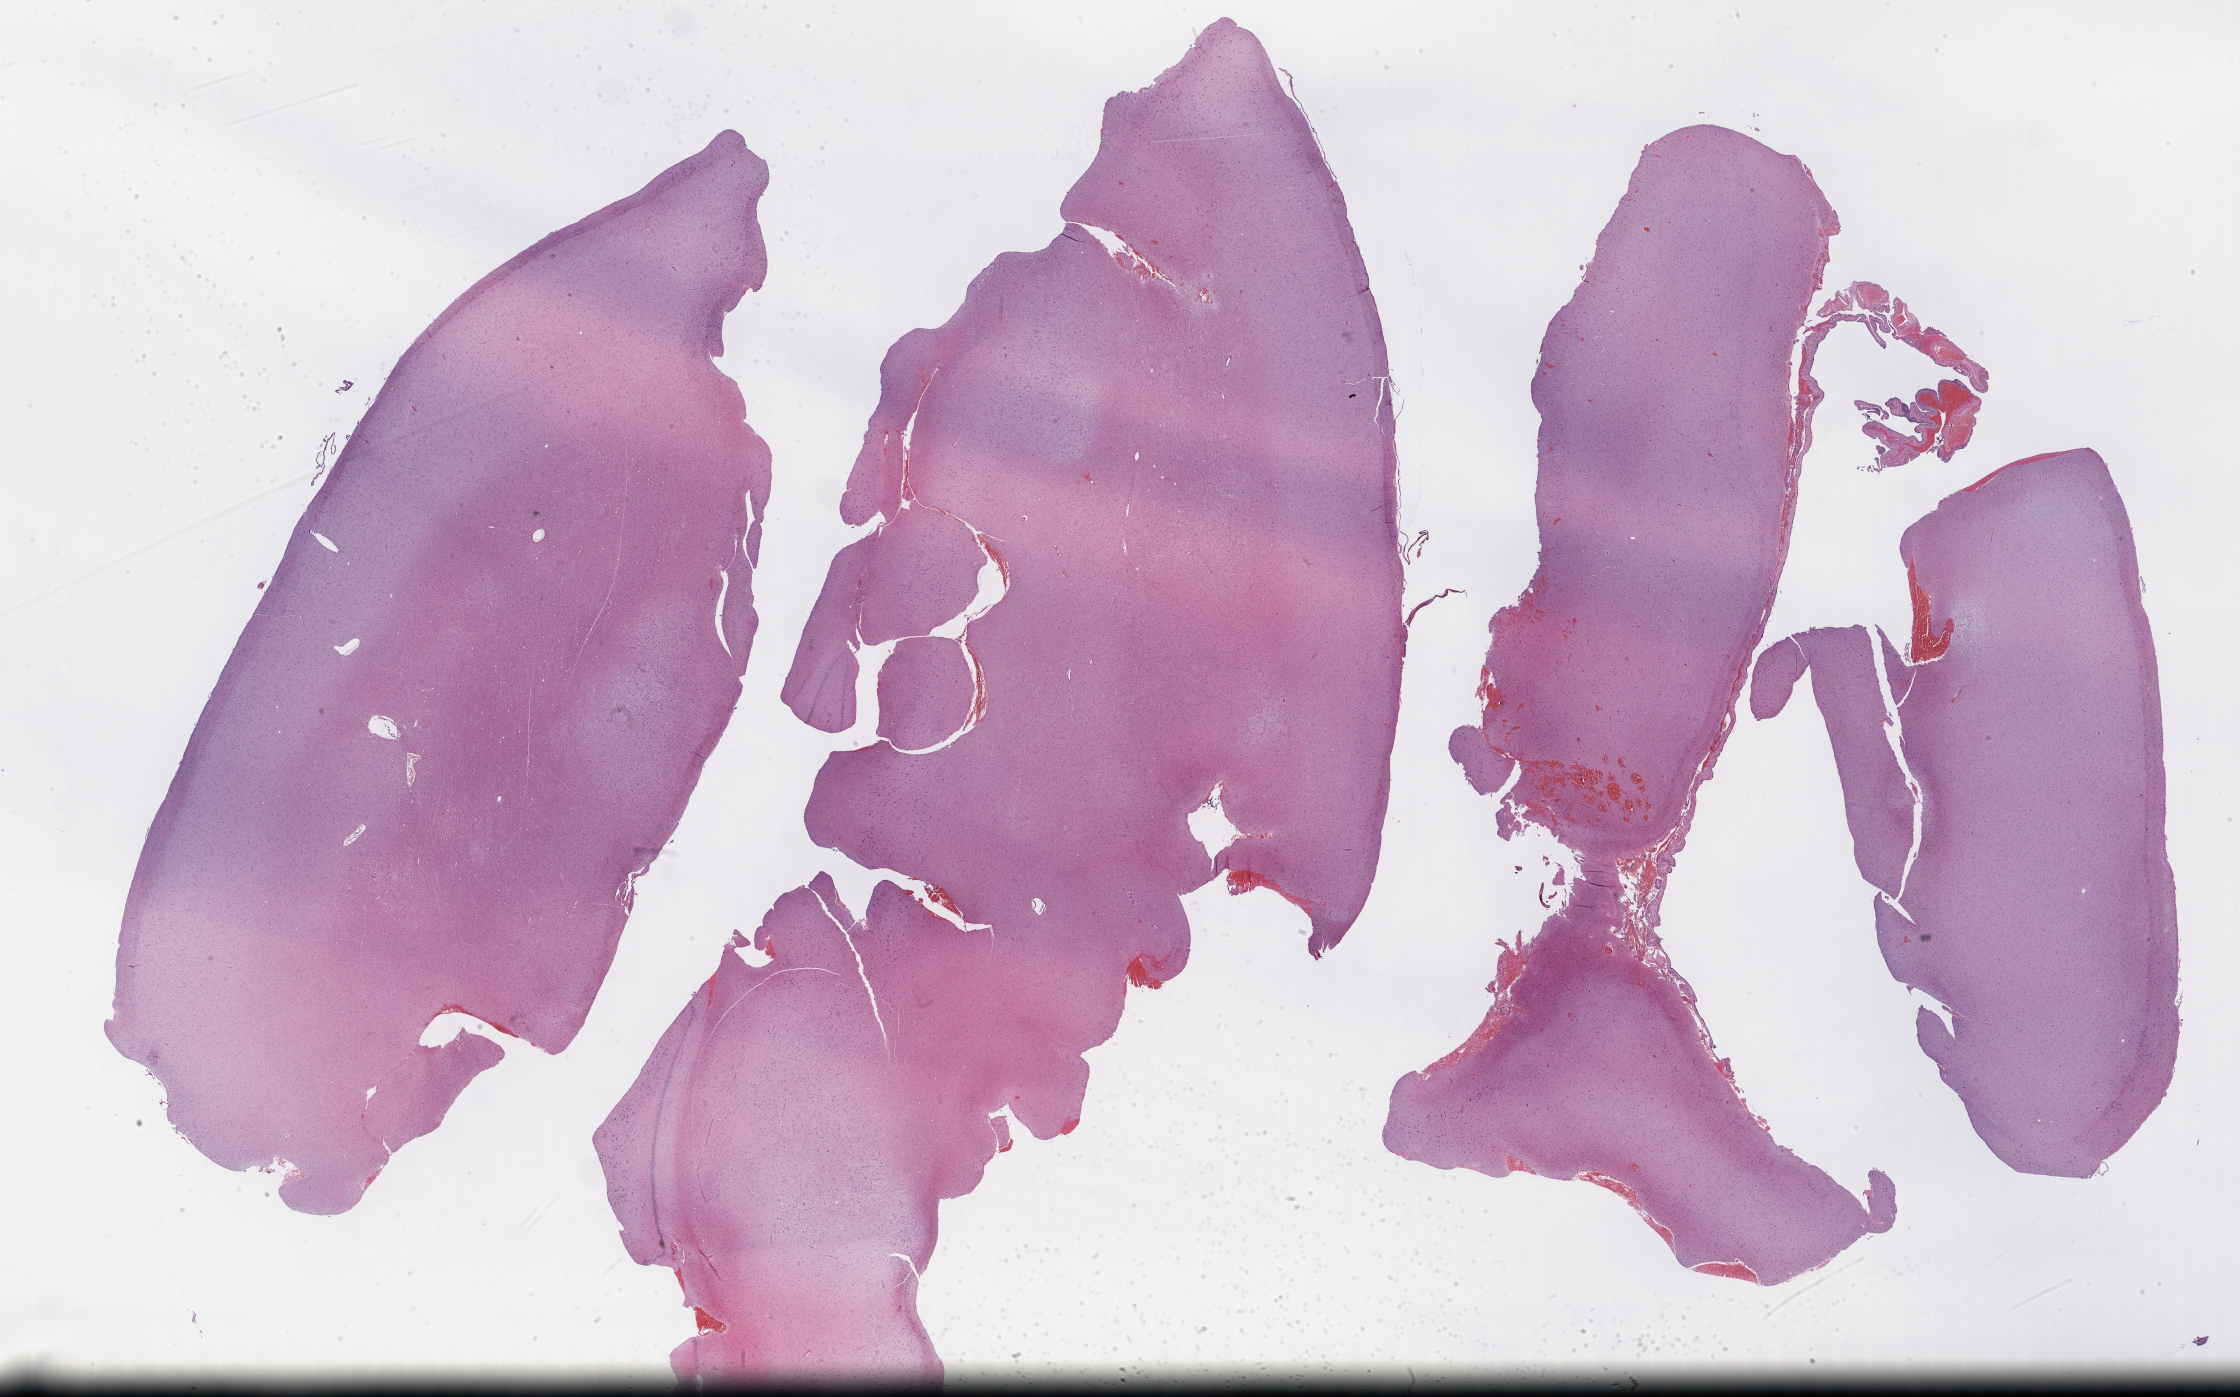
H&E-stained whole-slide image, whole scanned area (about 36.2 x 22.6 mm, from a 40x scan) shown as a low-resolution overview. Formalin-fixed paraffin-embedded (FFPE) diagnostic section. Brain, primary tumour sample. Female, age 37 years at initial diagnosis. Histologic grade: G2 (moderately differentiated).
* histologic diagnosis: Astrocytoma, NOS (cerebrum)